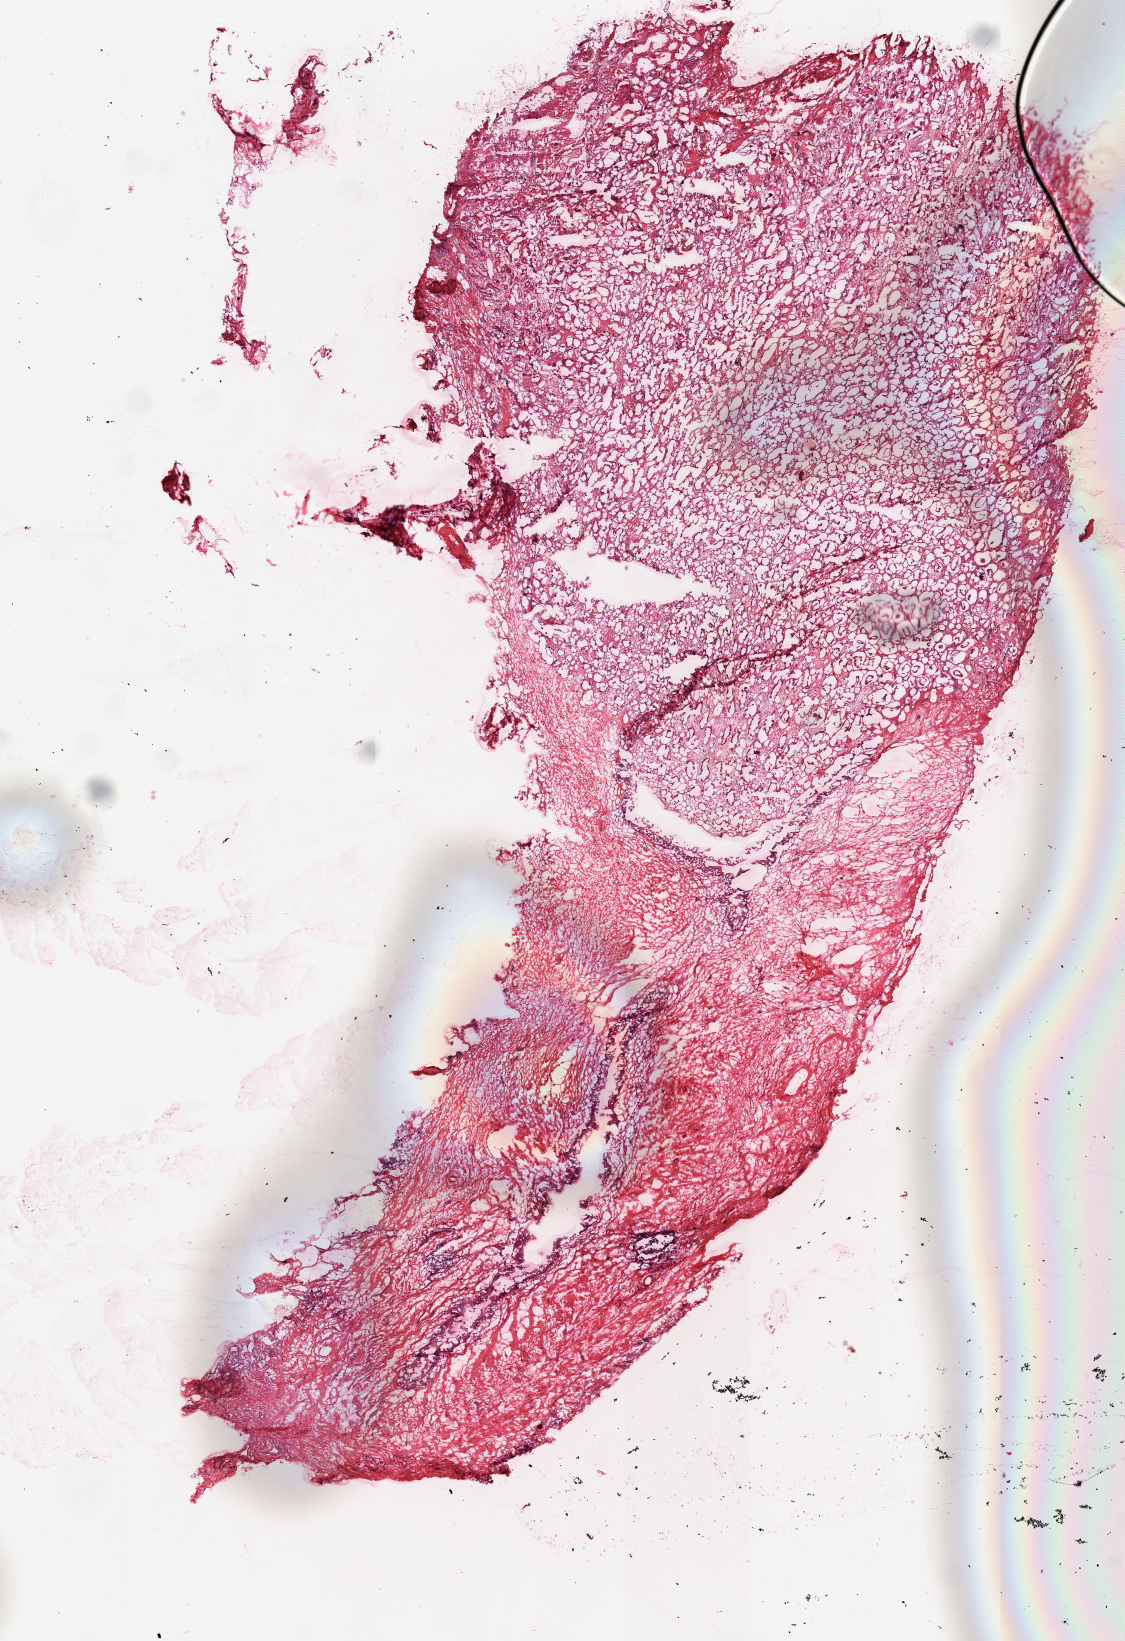
Whole-slide histology image, Hematoxylin and eosin (H&E) stained, low-resolution overview of the scanned area, about 8.9 x 13.0 mm (from a 20x scan); frozen section from the top of the tissue portion; sample: solid tissue normal (non-tumour tissue), kidney. Female, age 46 years at initial diagnosis.
This section: solid tissue normal sample (biorepository sample class). Patient diagnosis: Clear cell adenocarcinoma, NOS.